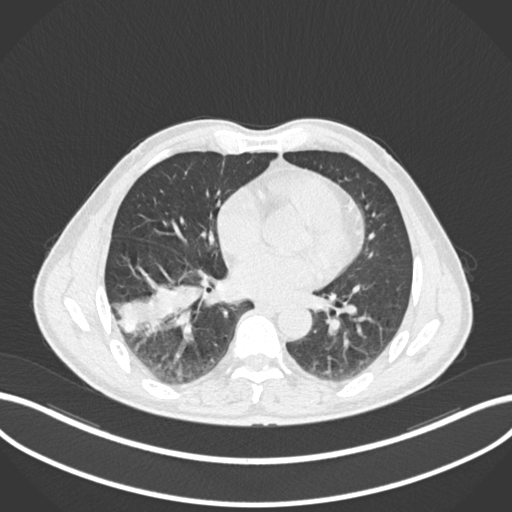
Chest CT, one axial slice. Position 81 of 208 along the scan axis. Reconstruction kernel B30f. Lung window (W 1500 / L -600 HU). 1 mm slice thickness. 512 × 512 image matrix. Patient: male, 58 years. Case-level facts recorded for this patient, not image findings: clinical TNM (as recorded): T3 N0 M0; histopathological grade: G2.
Structures marked on this image (rectangle marked by the reading radiologist):
- lung tumour (recorded histology: squamous cell carcinoma): bounding box (x1, y1, x2, y2) in pixels: (112, 276, 203, 340)